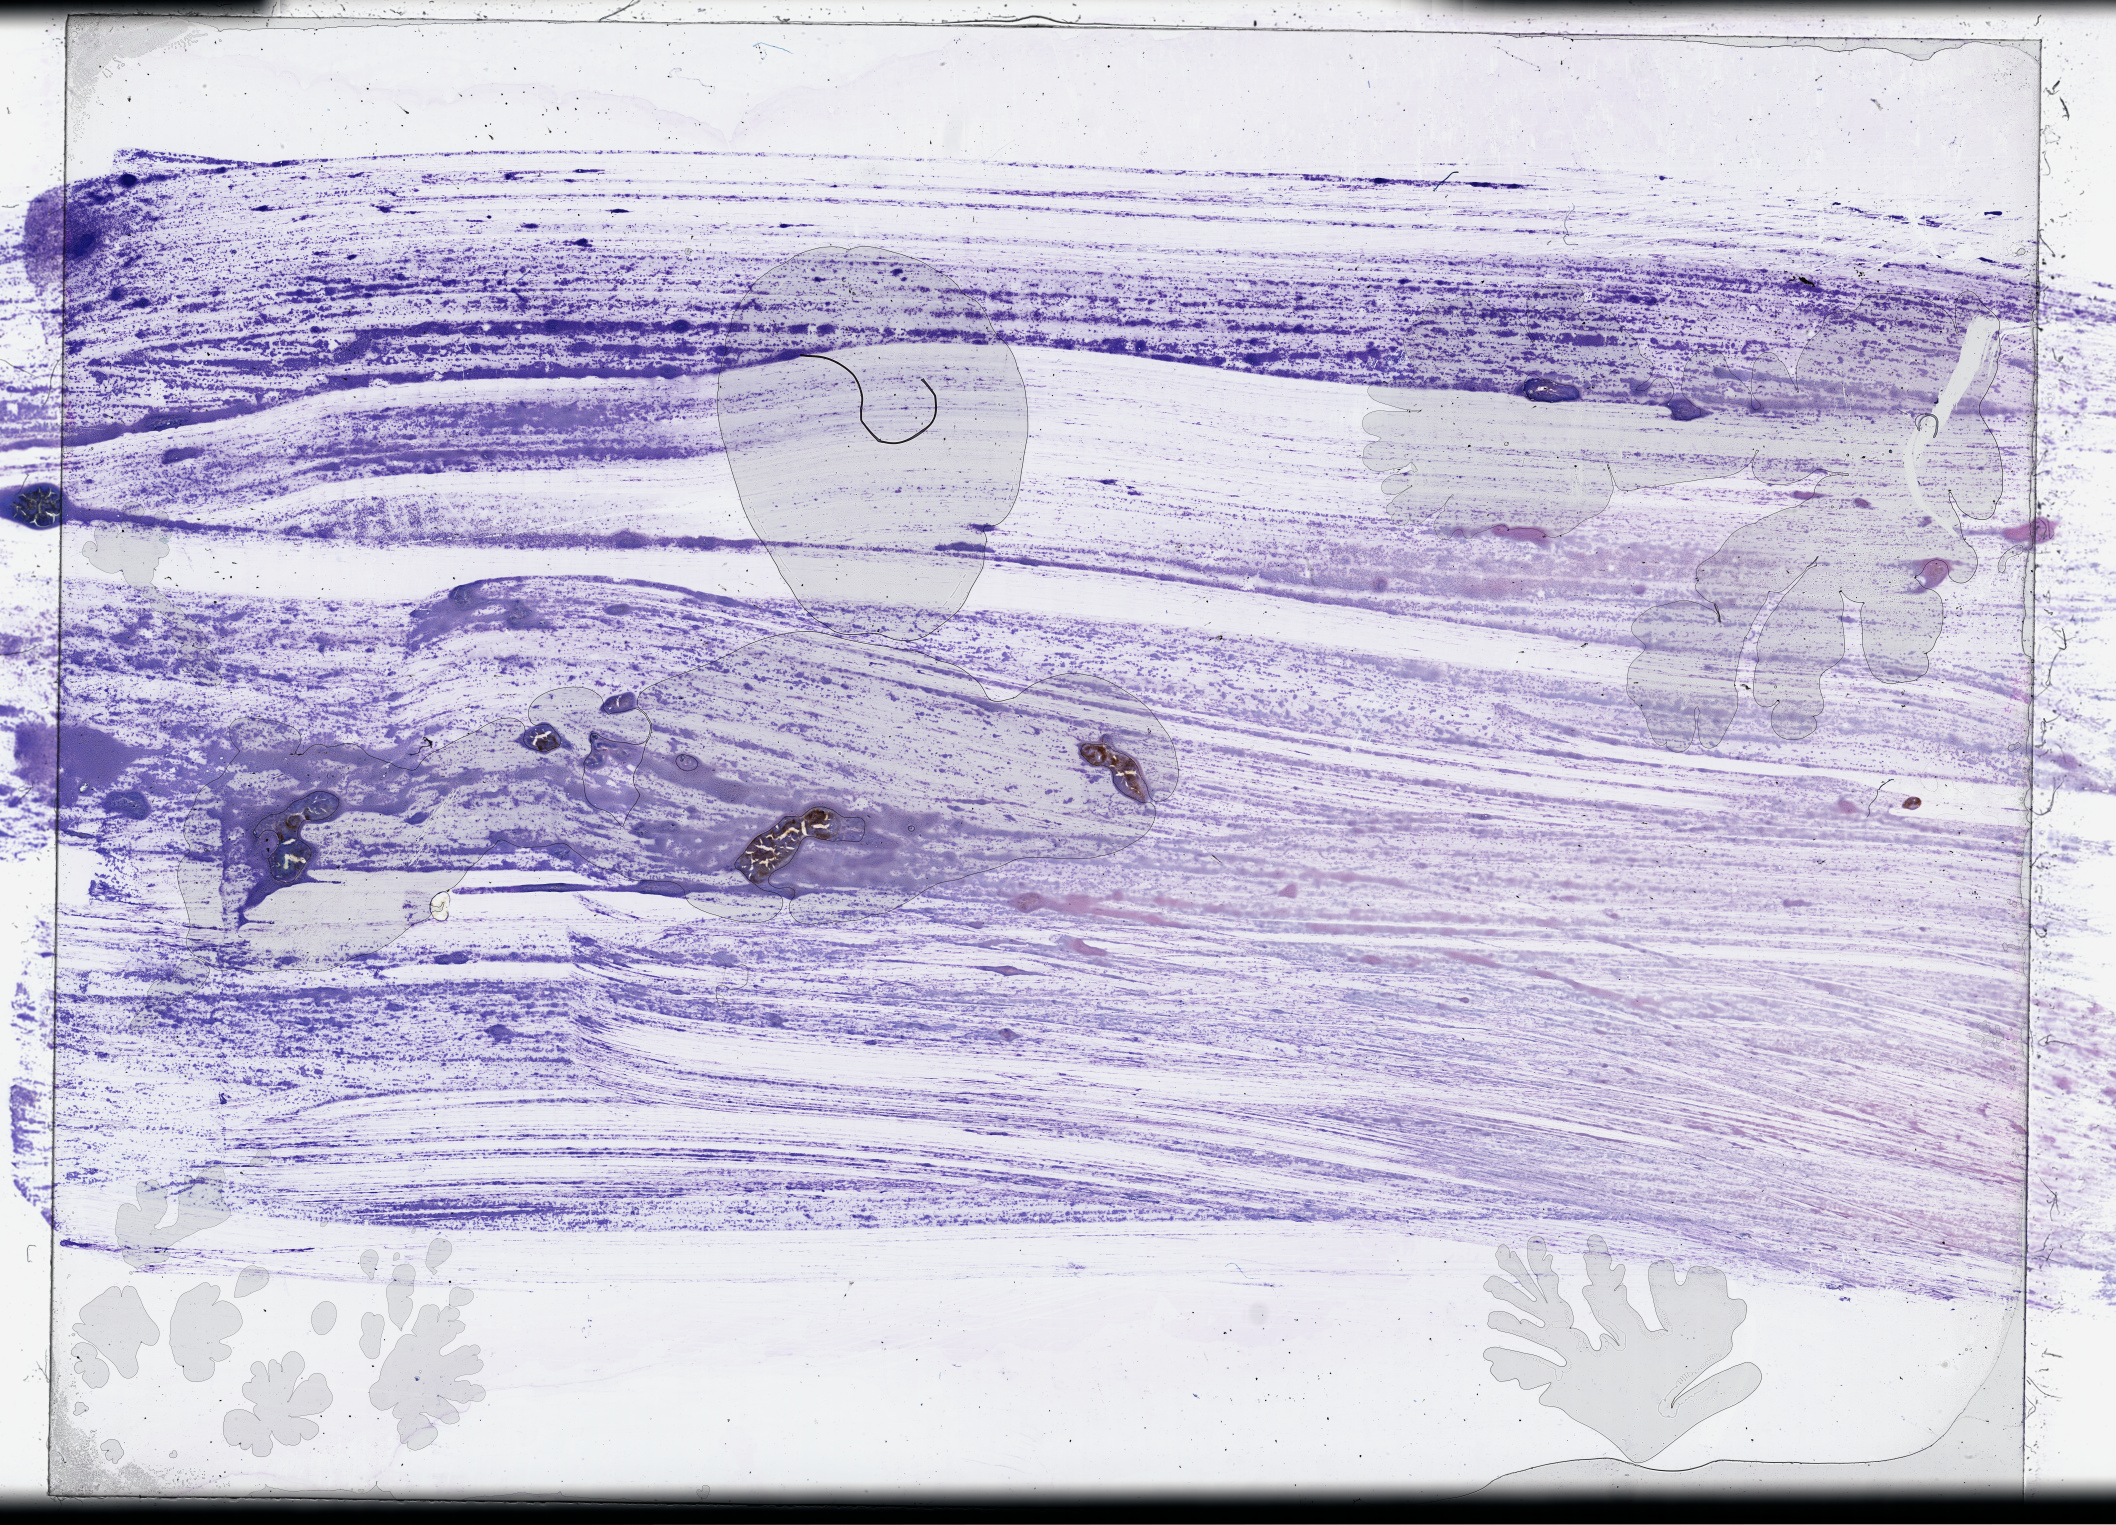
Whole-slide histology image, Hematoxylin and eosin (H&E) stained — low-resolution overview of the scanned area, about 34.2 x 24.6 mm (from a 40x scan). Bone marrow (leukaemic) sample. 60-year-old male patient. Blasts: 90%.
Diagnosis: Acute Myeloid Leukemia. FAB classification: M4.